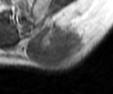
MRI of an extremity soft-tissue mass, one axial slice; MR volume resampled by the dataset authors to the PET/CT grid (not the native acquisition matrix); 113 × 94 image matrix, field of view 110 × 92 mm. Male patient. From the clinical record (not read from this slice): histological type: leiomyosarcoma; grade: intermediate; site of the primary tumour: left pelvis.
Outlined on this slice (expert contour drawn on MRI and transferred to this co-registered scan by the dataset authors):
- gross tumour volume (mass): box from (x=26, y=20) to (x=87, y=69) px